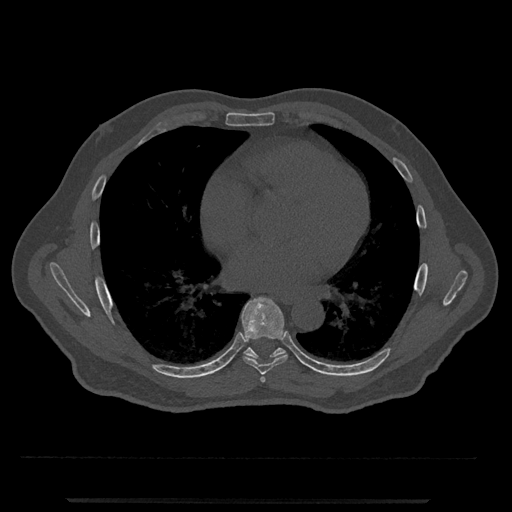
CT including the spine, one axial slice. Slice 664 of 797 in the series (ordered by position). Reconstruction kernel Br40s/3. Bone window (W 1800 / L 400 HU). 512 × 512 image matrix, field of view 419 × 419 mm. Patient: male, 63 years. Case-level facts recorded for this patient, not image findings: primary cancer: prostate.
Structures marked on this image (semi-automatic segmentation, software-assisted and operator-edited):
- T6 vertebra: box from (x=260, y=375) to (x=266, y=383) px
- T7 vertebra: (x=242, y=297)–(x=288, y=375)
- T8 vertebra: (x=244, y=347)–(x=286, y=359)